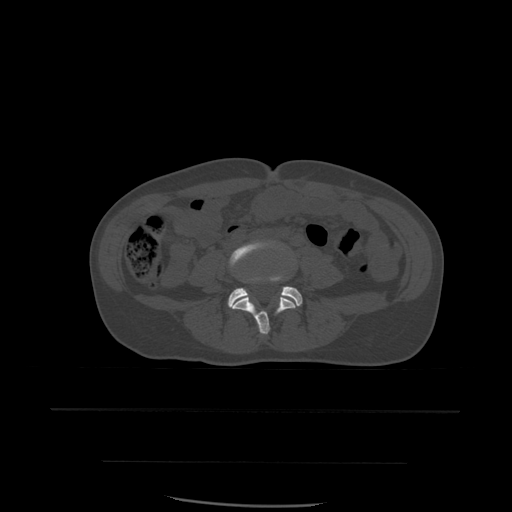
CT including the spine, one axial slice; position 161 of 574 along the scan axis; bone window (W 1800 / L 400 HU); 1.25 mm slice thickness; 512 × 512 image matrix. Patient age 48 years. From the clinical record (not read from this slice): primary cancer: lung.
Annotated regions visible in this slice (semi-automatic segmentation, software-assisted and operator-edited):
- L4 vertebra: bounding box [x1, y1, x2, y2] px = [229, 241, 296, 335]
- L5 vertebra: [228, 277, 303, 308]